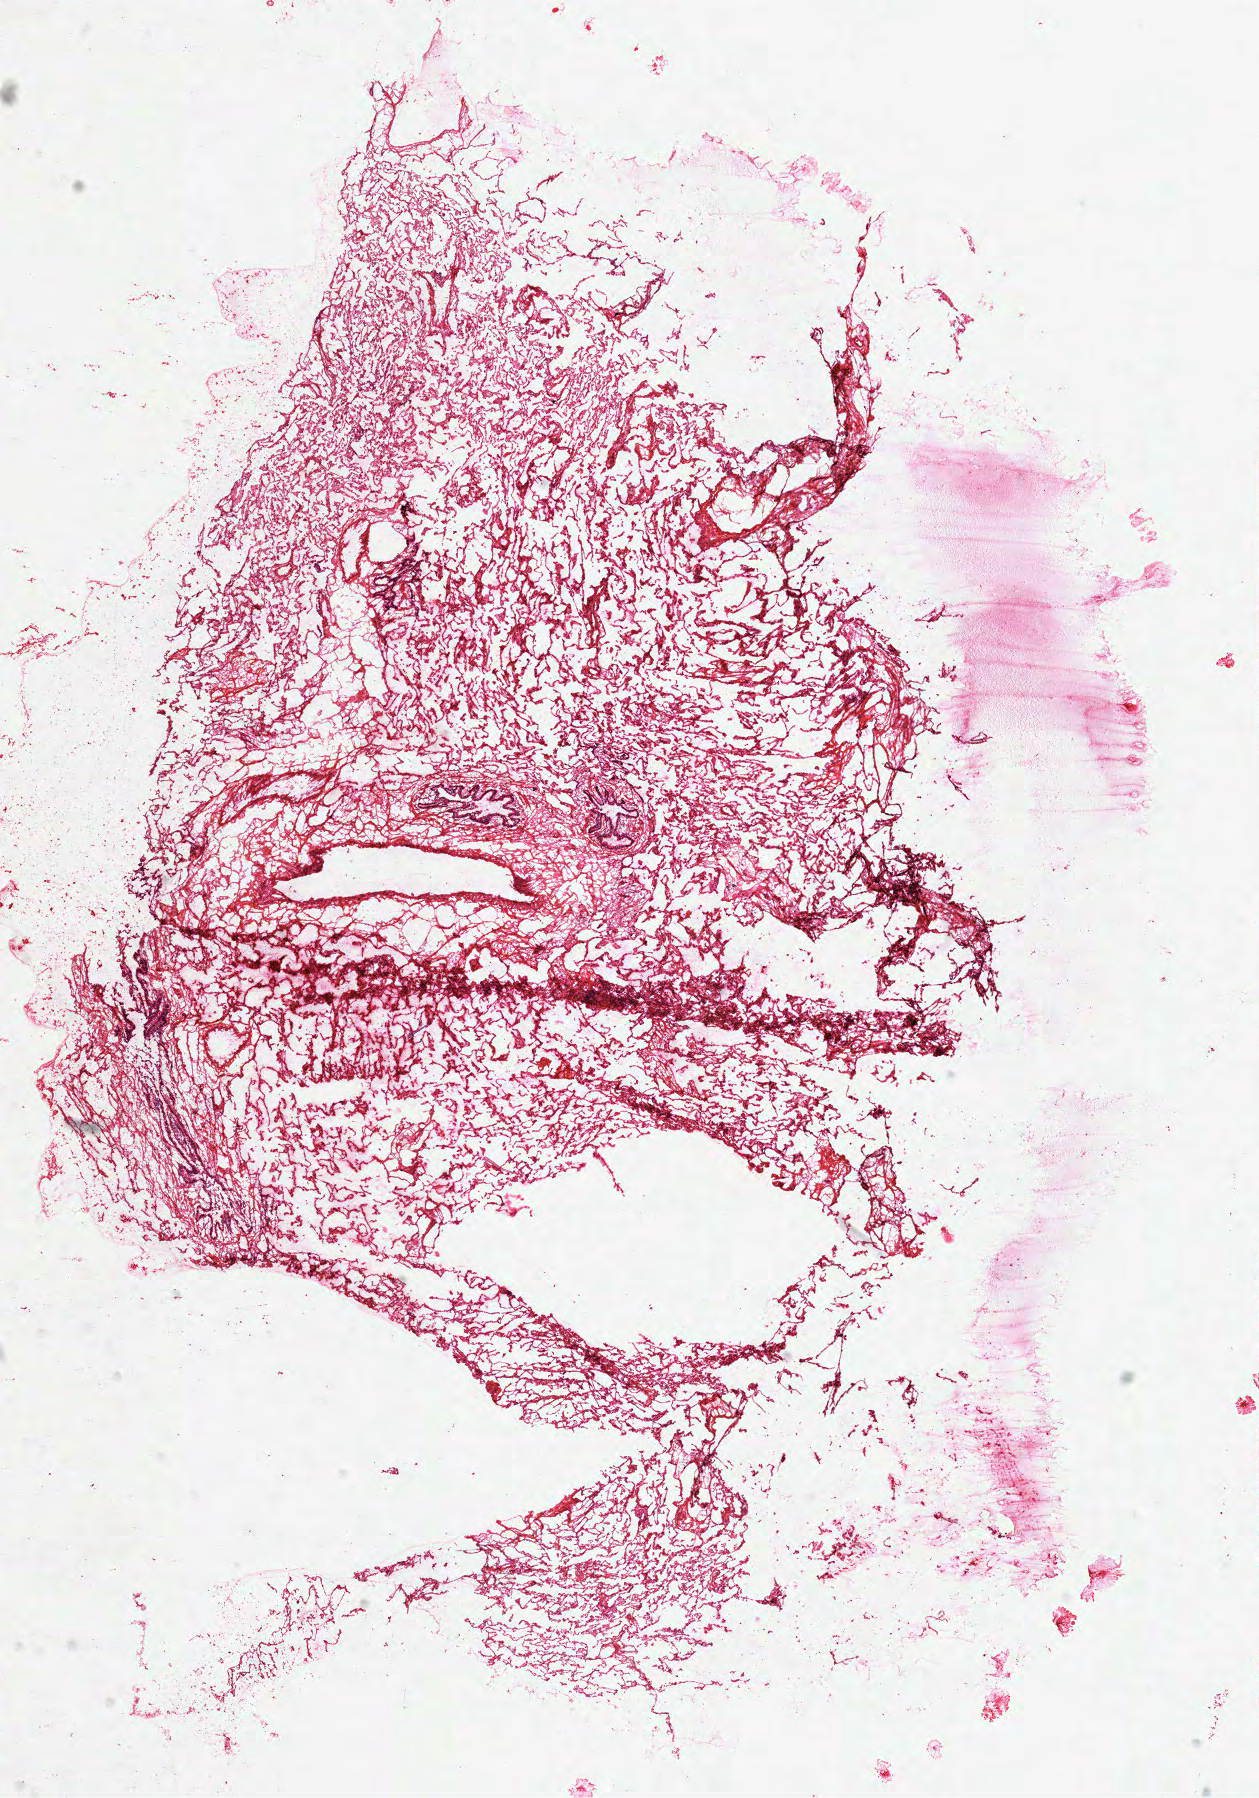
Digitized Hematoxylin and eosin (H&E) stained tissue section (whole slide), a low-resolution overview of the entire scanned area, about 10.2 x 14.5 mm (acquisition: 40x scan); frozen section from the top of the tissue portion; sample: solid tissue normal (non-tumour tissue), lung. Male, age 68 years at initial diagnosis.
This section: solid tissue normal (non-tumour) sample from the same patient. Patient diagnosis: Mucinous adenocarcinoma (lower lobe, lung).